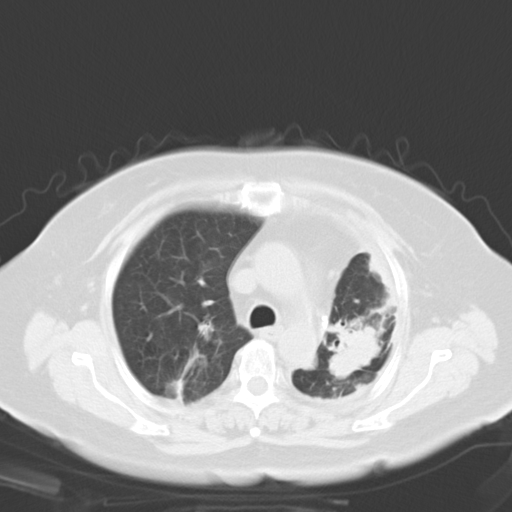
Chest CT, one axial slice; slice 21 of 29 in the series (ordered by position); 120 kVp; lung window (W 1500 / L -600 HU); 8 mm slice thickness; 512 × 512 image matrix, field of view 347 × 347 mm. Patient: female, 69 years. From the clinical record (not read from this slice): clinical TNM (as recorded): T3 N0 M0.
Structures marked on this image (rectangle marked by the reading radiologist):
- lung tumour (recorded histology: adenocarcinoma): bounding box (x1, y1, x2, y2) in pixels: (322, 318, 381, 380)